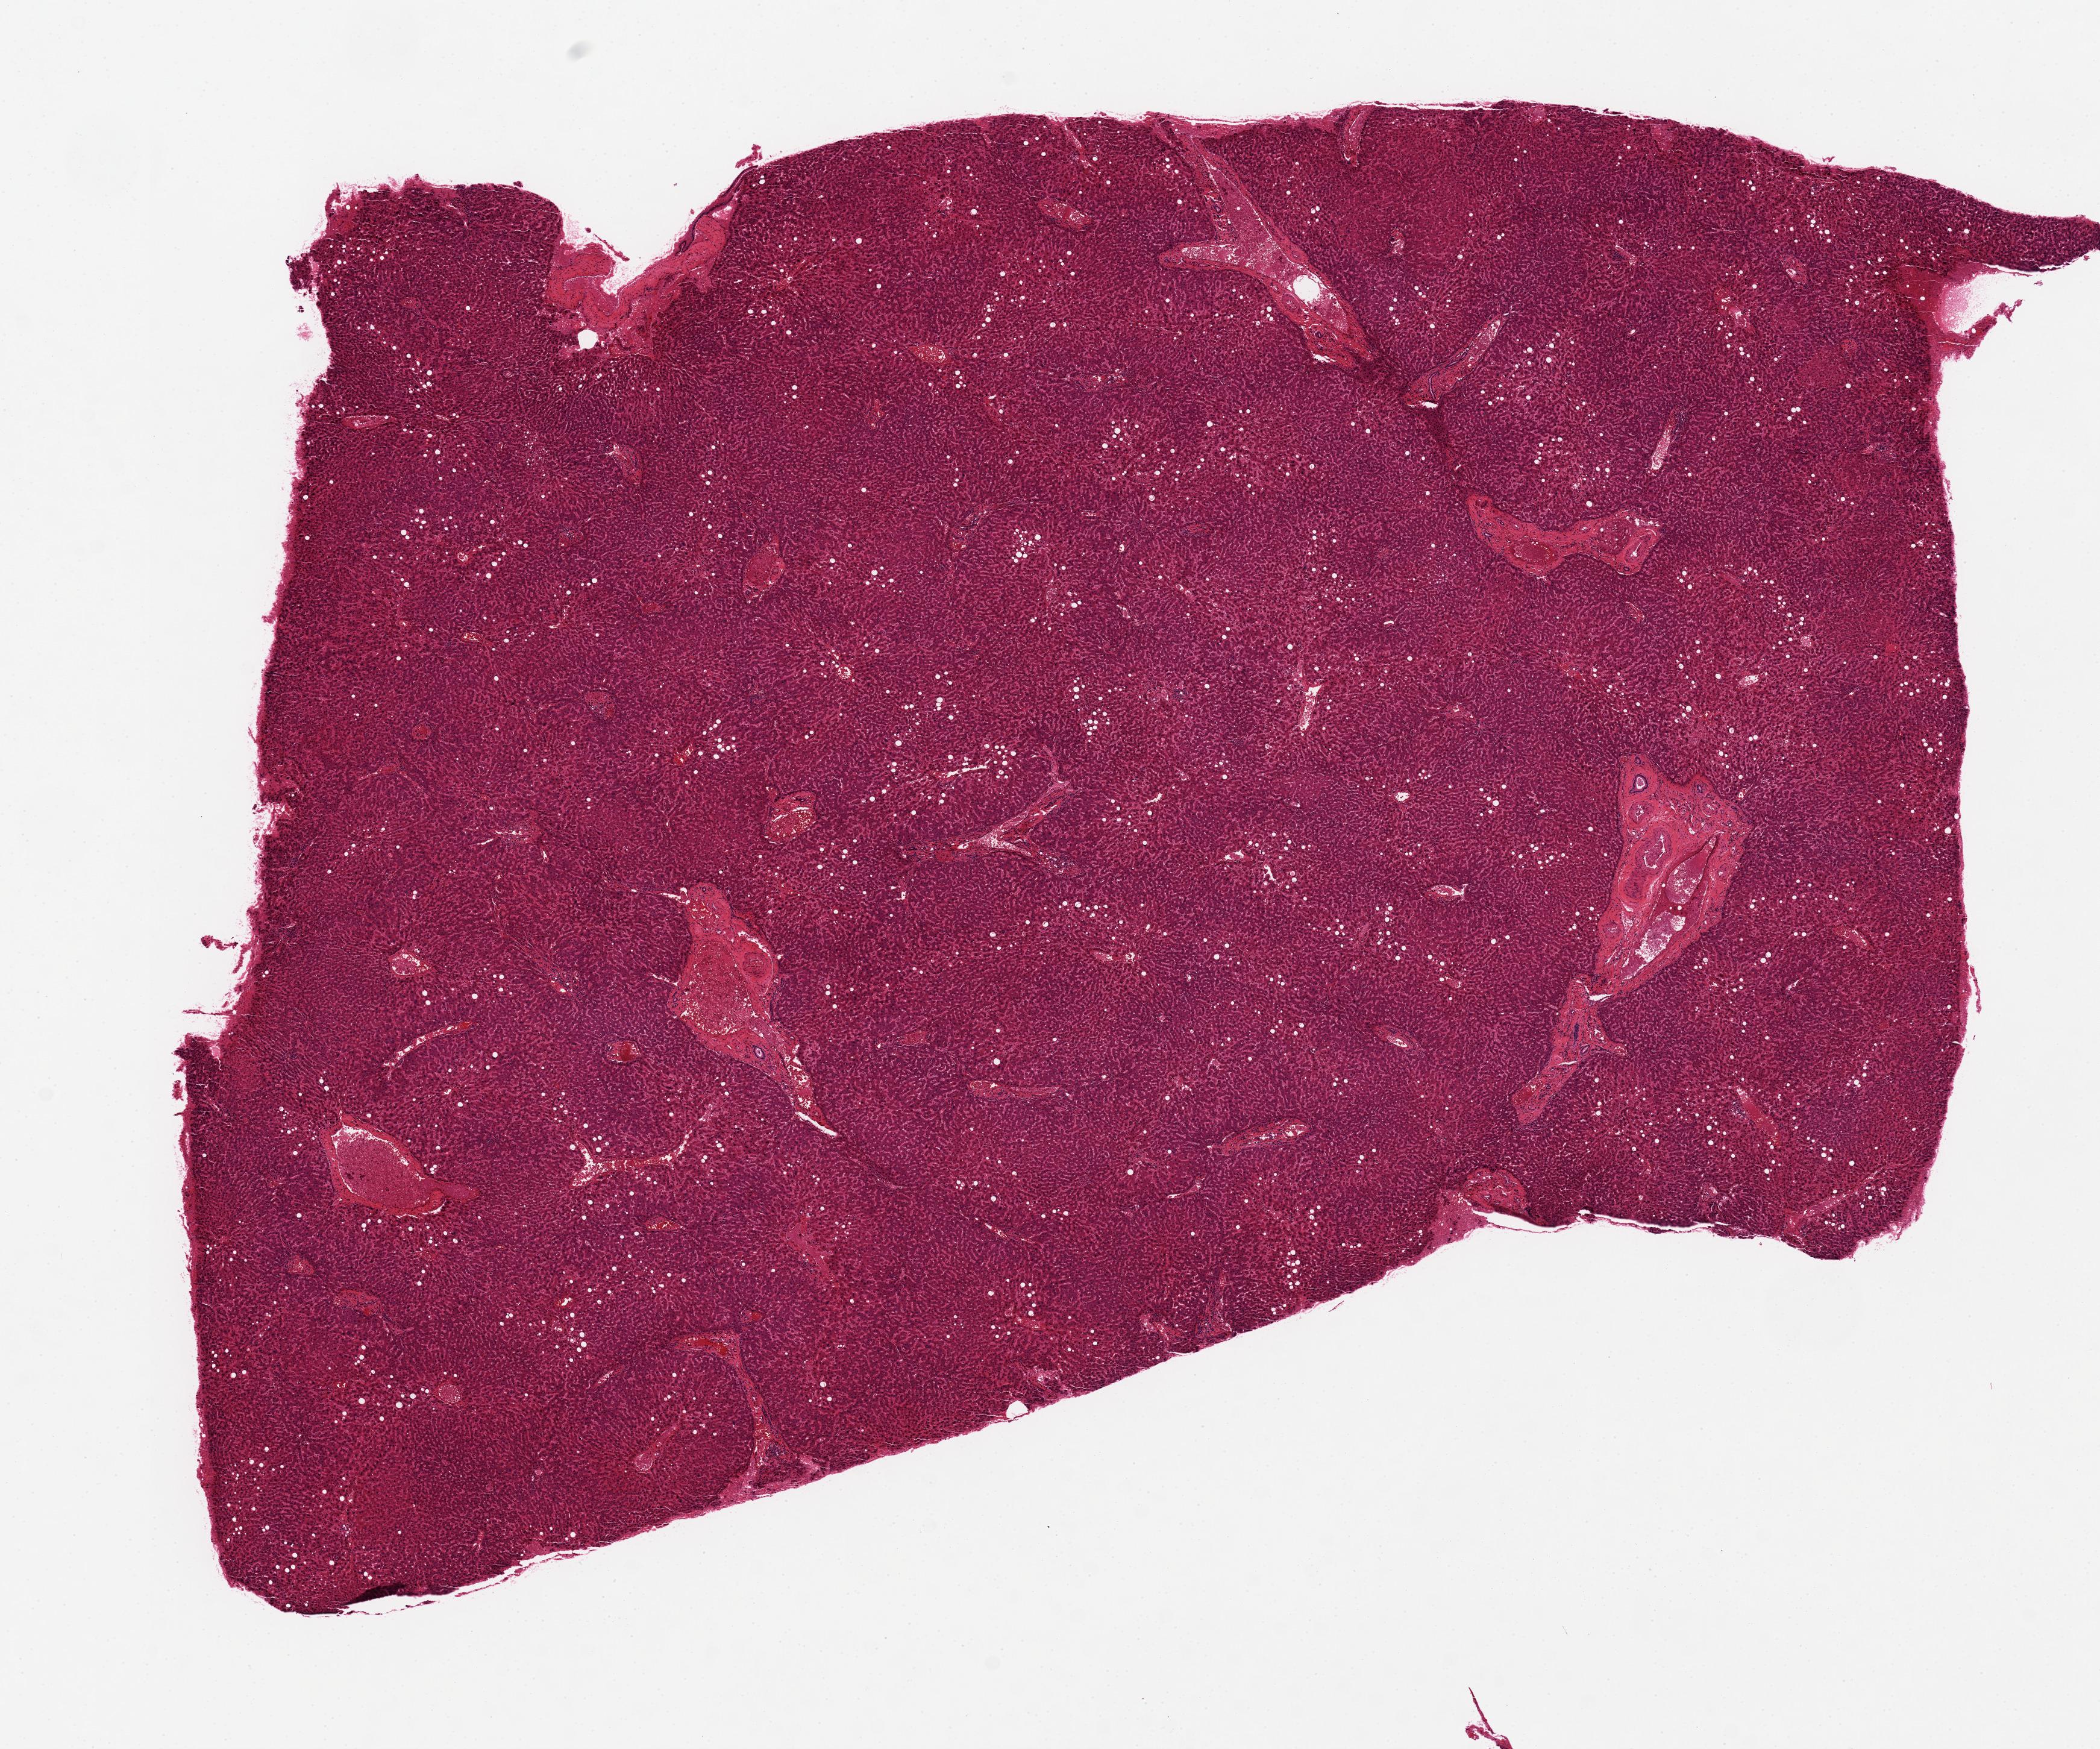
Digitized hematoxylin and eosin (H&E)-stained section, shown as a low-resolution overview of the whole scanned area (about 13.8 x 11.5 mm, slide scanned at 20x), PAXgene-fixed paraffin-embedded (PFPE) section, sampled site (target tissue): liver, tissue donor sample. Male donor.
• review note (as recorded): 11.2x 8.3mm. About 10% macrovesicular steatosis